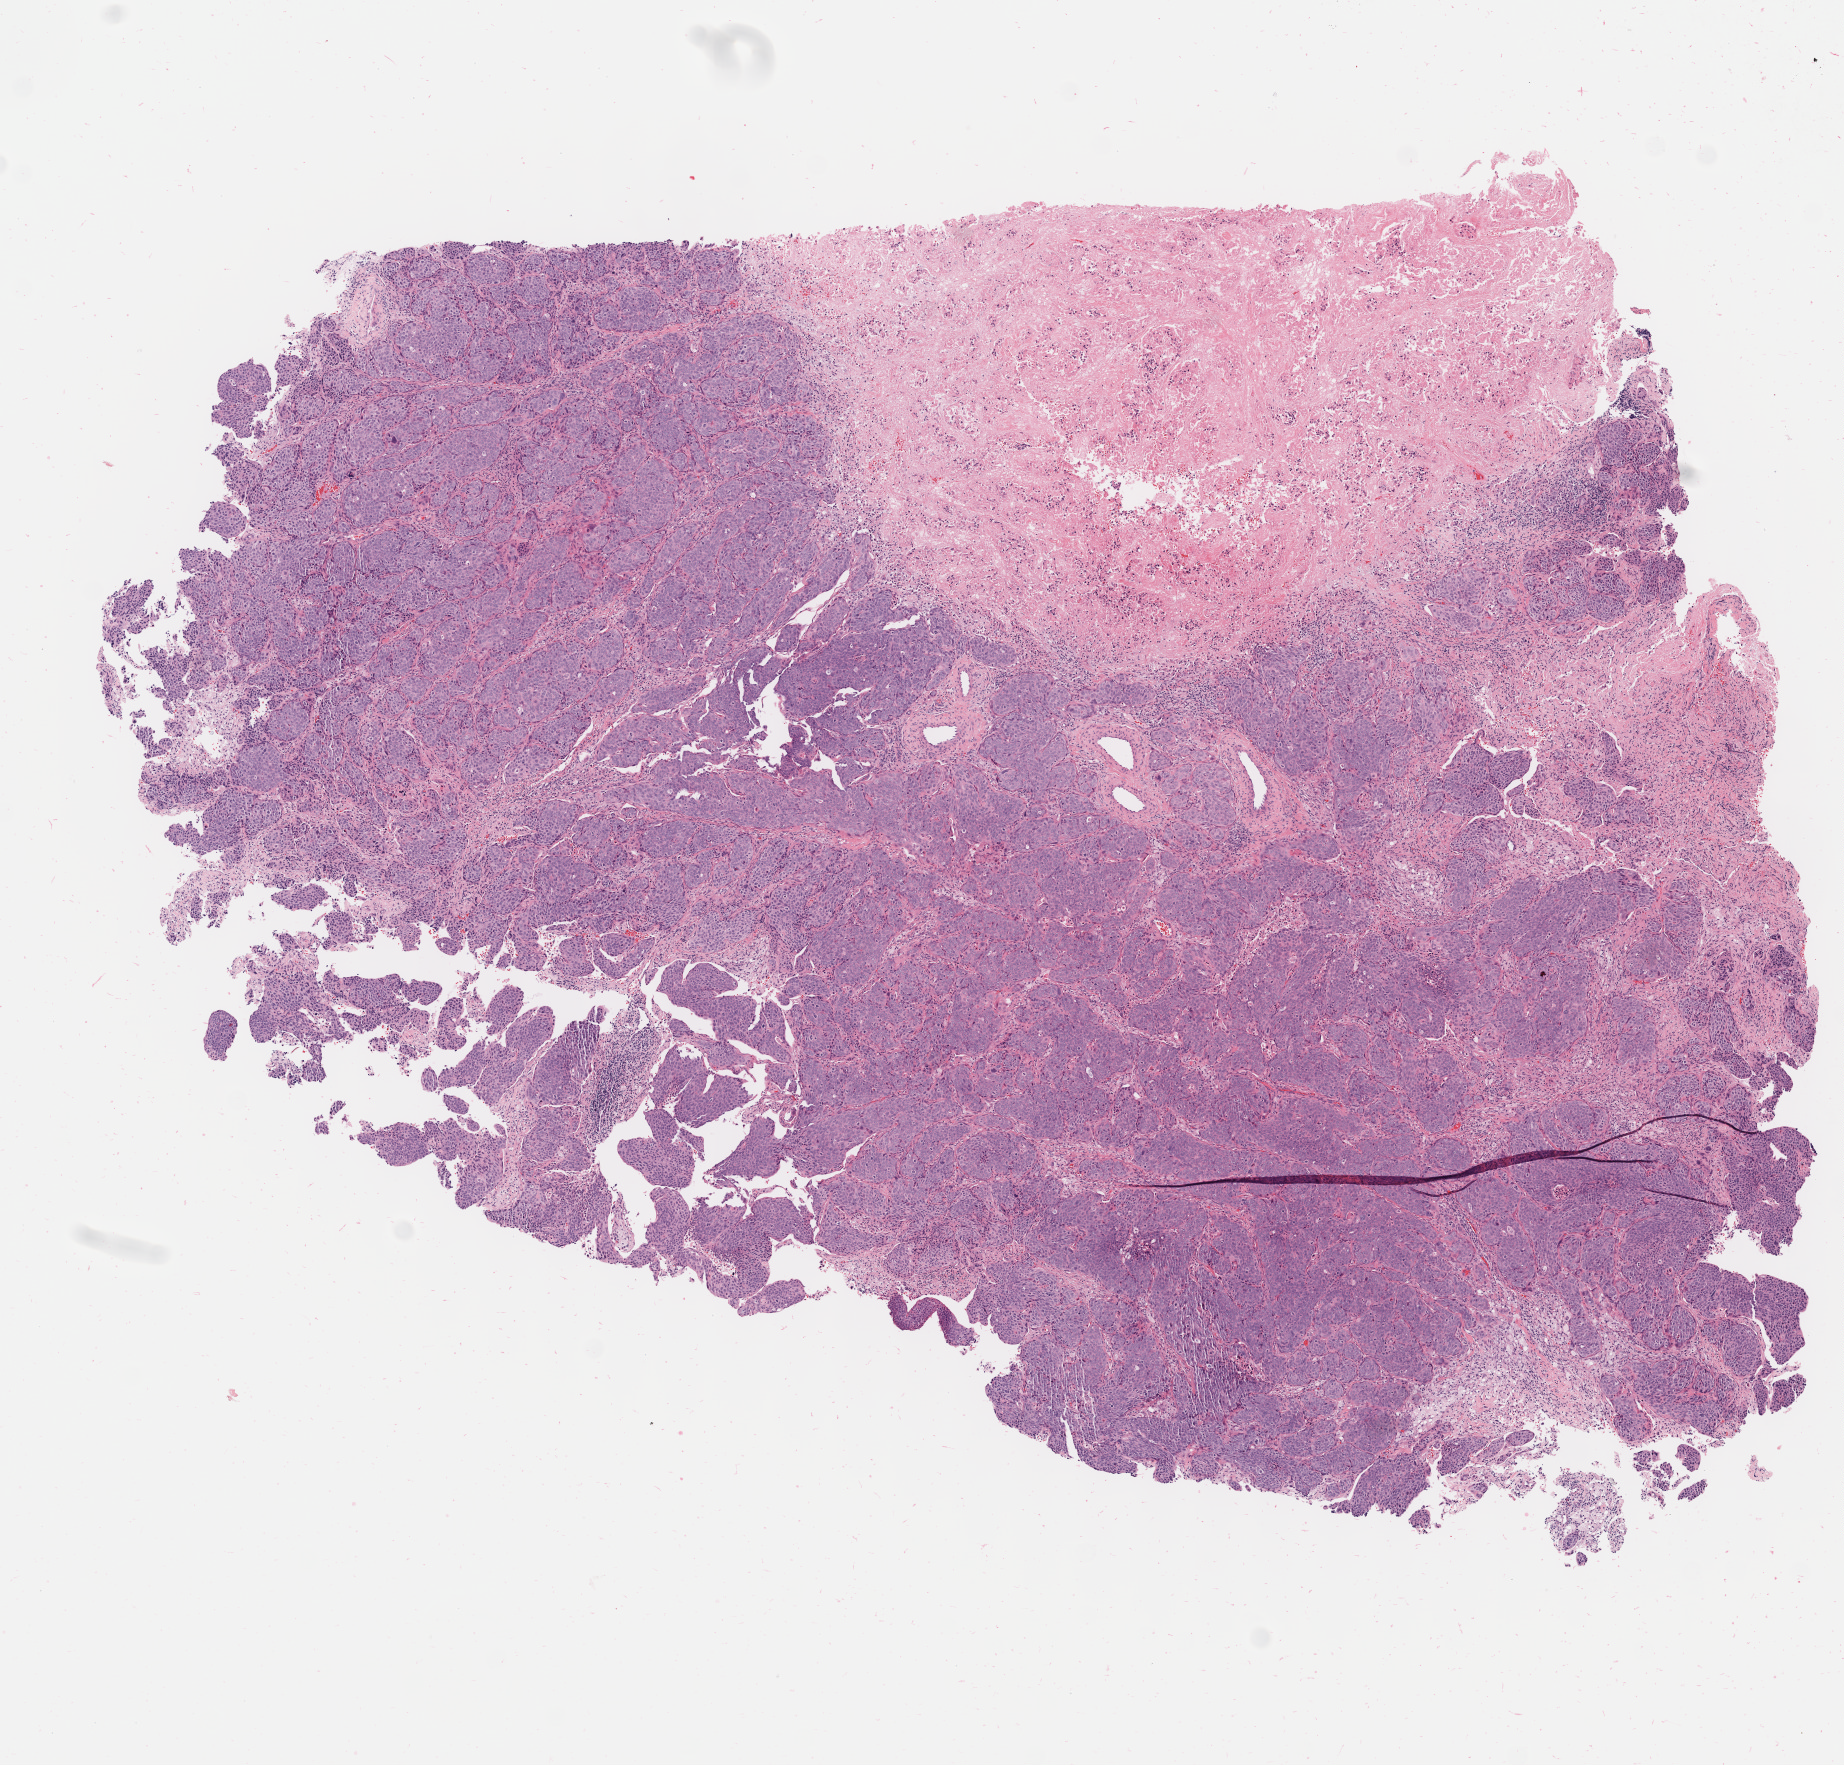
Whole-slide image, H&E stain — low-resolution overview of the scanned area, about 7.3 x 7.0 mm, tumor tissue, anatomic site: cervix. Female patient, age 53 years.
Histologic diagnosis: Squamous cell carcinoma, large cell, nonkeratinizing, NOS.